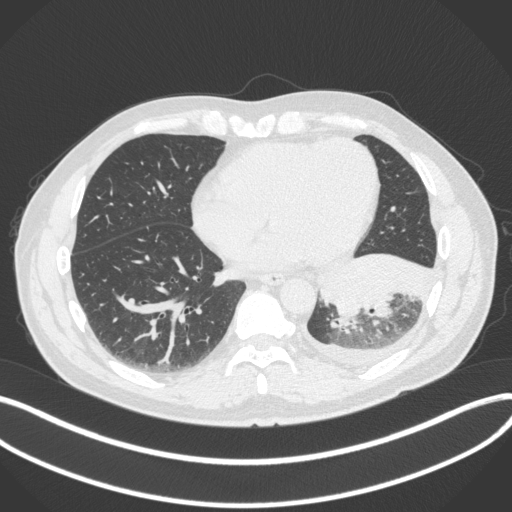
Chest CT, one axial slice; slice 124 of 350 in the series (ordered by position); reconstruction kernel B31f; 120 kVp; lung window (W 1500 / L -600 HU); 512 × 512 image matrix, field of view 400 × 400 mm. Male patient, age 58 years. Case-level facts recorded for this patient, not image findings: clinical TNM (as recorded): T3 N1 M1b.
Annotated regions visible in this slice (bounding box drawn by a radiologist):
- lung tumour (recorded histology: small cell carcinoma): bounding box <320,254,434,325> (left, top, right, bottom; pixels)